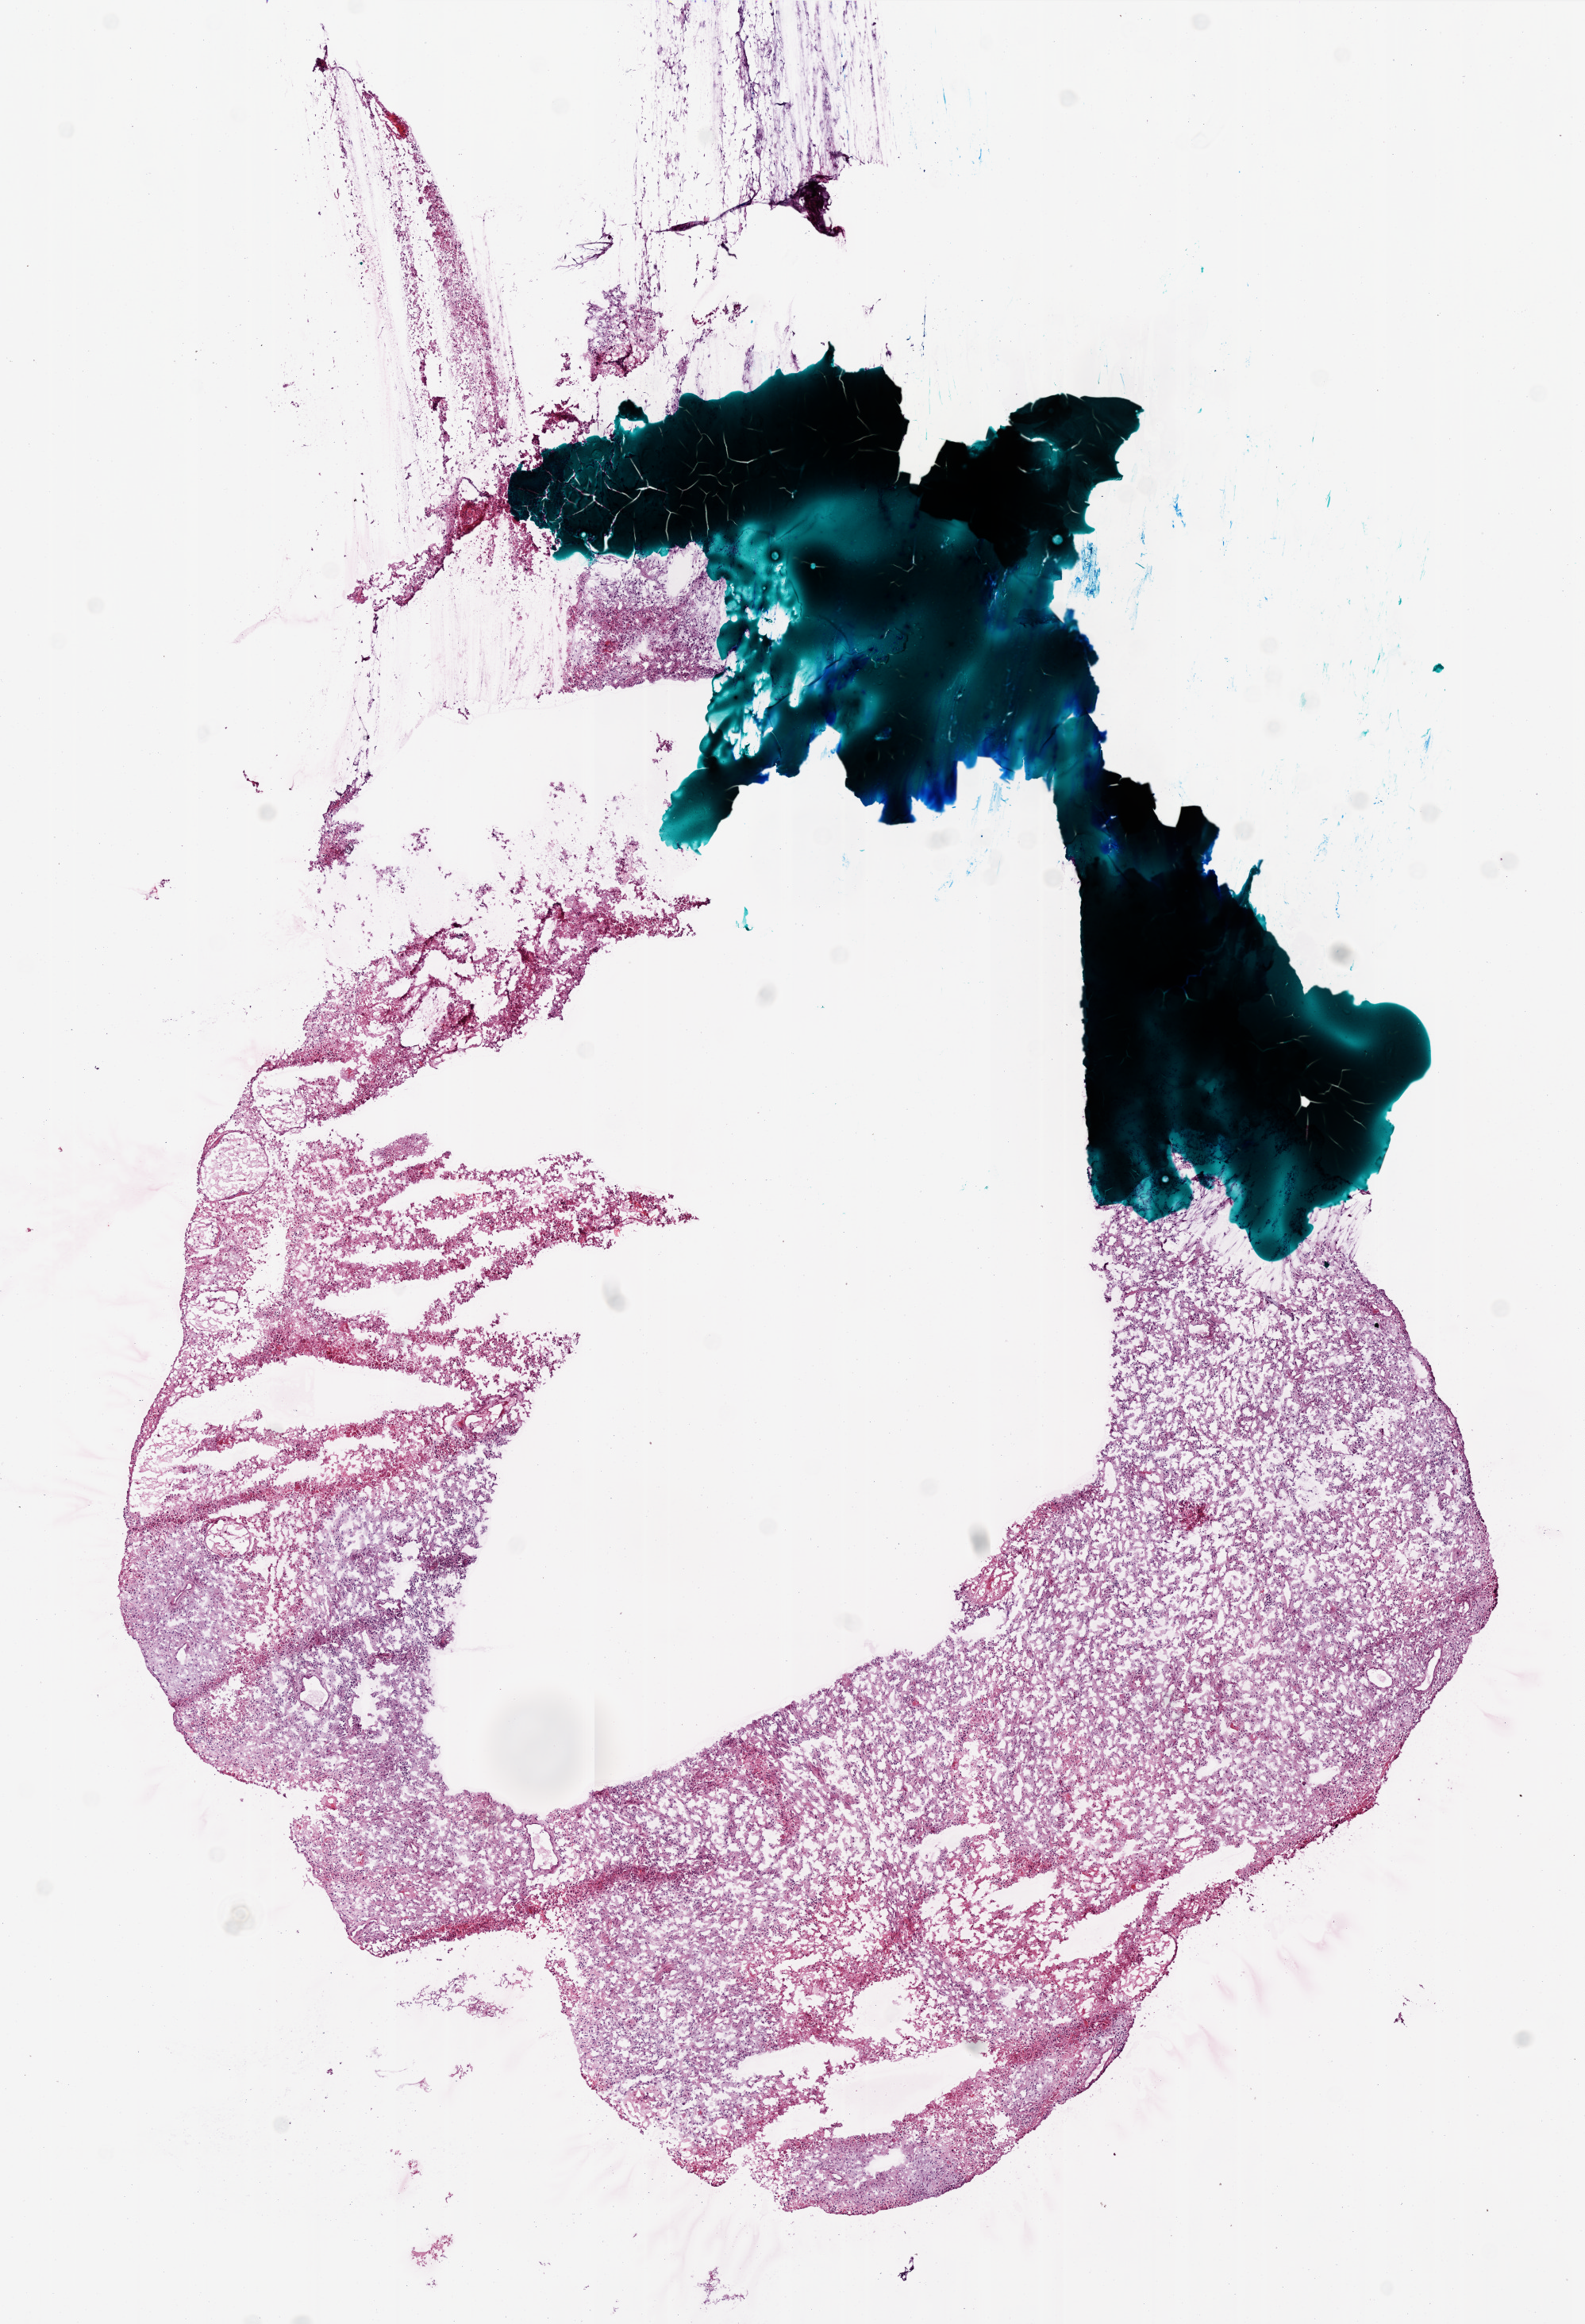
H&E whole-slide image, whole scanned area (about 8.0 x 11.7 mm, slide scanned at 20x) shown as a low-resolution overview. Frozen section from the bottom of the tissue portion. Brain, primary tumour sample. Patient: male, age at initial diagnosis 14 years. Pathologist review of this section (percent, as recorded): tumour cells 75%, tumour nuclei 100%, normal cells 0%, stromal cells 0%, necrosis 25%. Inflammatory infiltration, as recorded: lymphocyte infiltration 0%.
- histologic diagnosis: Glioblastoma